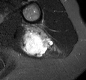
MRI of an extremity soft-tissue mass, one axial slice. Position 10 of 30 along the scan axis. STIR. MR volume resampled by the dataset authors to the PET/CT grid (not the native acquisition matrix). 86 × 80 image matrix, field of view 84 × 78 mm. Female patient. From the clinical record (not read from this slice): histological type: malignant fibrous histiocytoma; grade: low; site of the primary tumour: left arm.
Structures marked on this image (expert contour drawn on MRI and transferred to this co-registered scan by the dataset authors):
- gross tumour volume (mass): bounding box <19,26,55,57> (left, top, right, bottom; pixels)